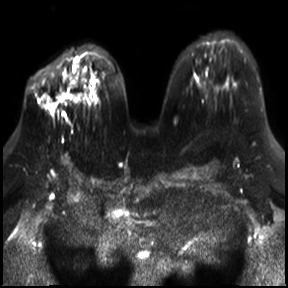
Breast MRI, one axial slice. Slice 18 of 30 in the series (ordered by position). Diffusion-weighted series; image 2 of 4 stored at this slice position (different b-values; order by instance number). 3 T. 4 mm slice thickness. 288 × 288 image matrix. Female patient.
Outlined on this slice (manually delineated by an expert):
- tumour on diffusion-weighted imaging: bounding box <41,102,57,112> (left, top, right, bottom; pixels)